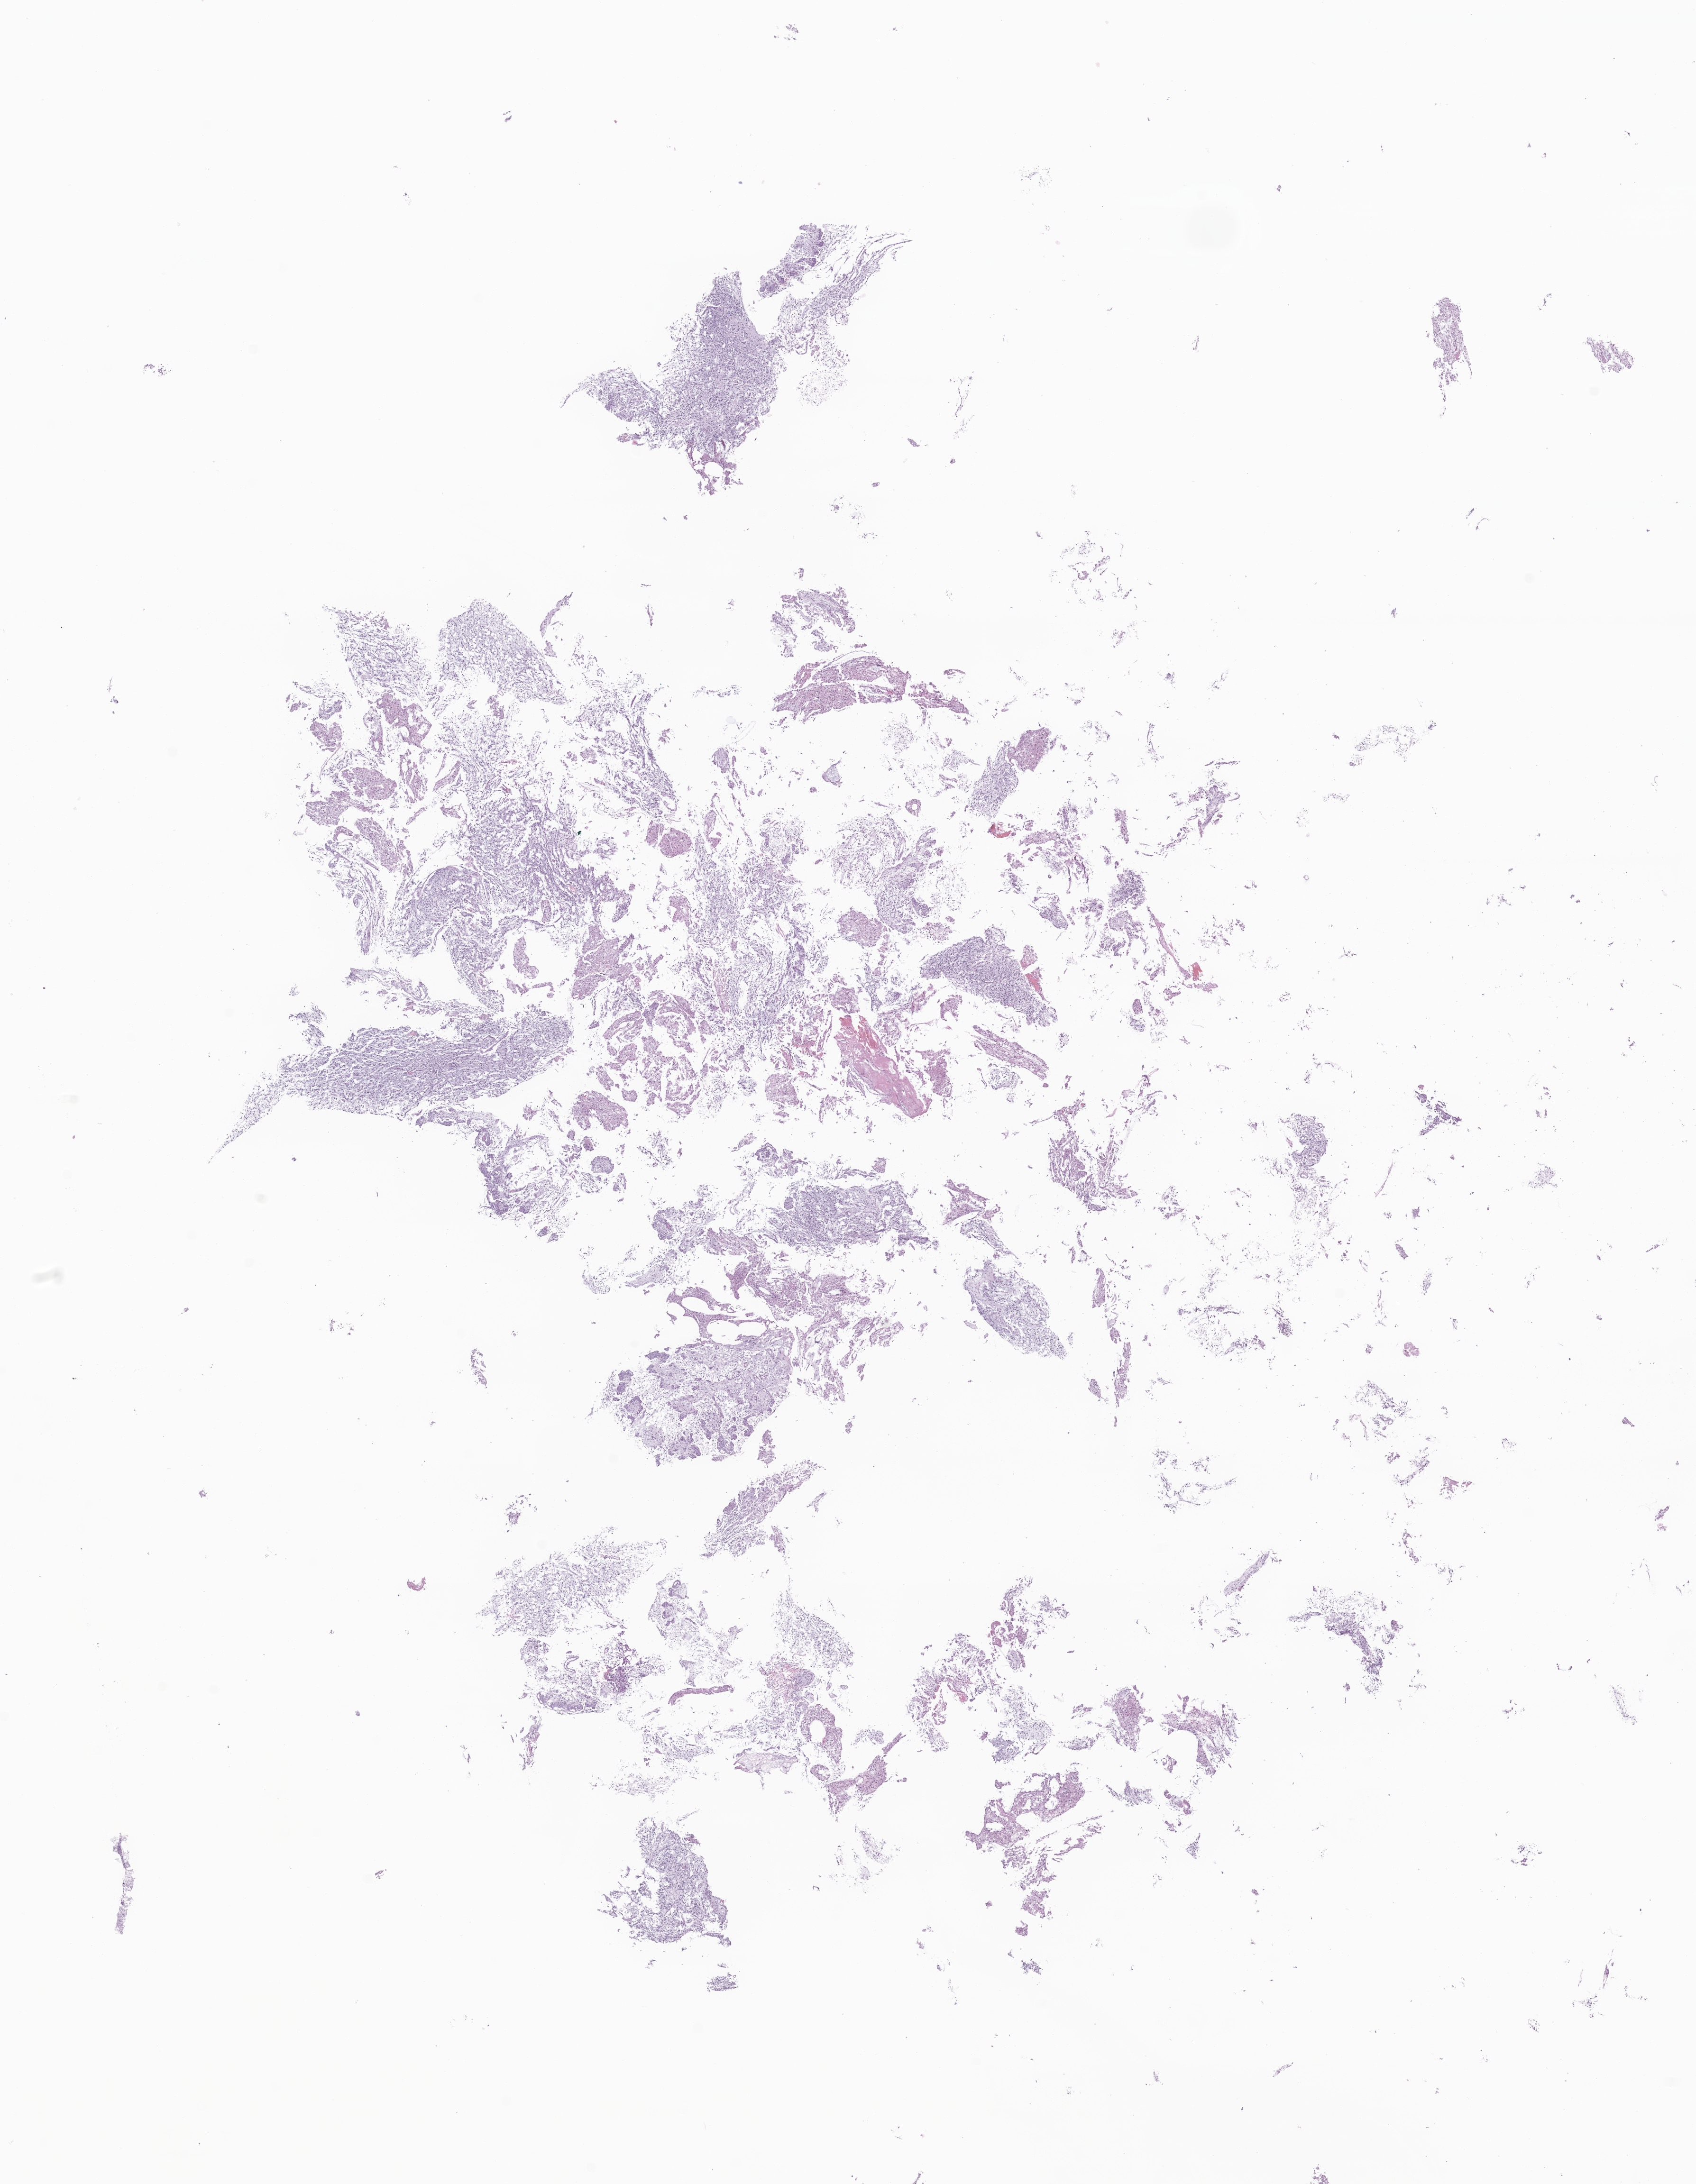
H&E whole-slide image of tumor tissue from the spinal cord, whole scanned area (about 15.1 x 19.4 mm) shown as a low-resolution overview. Formalin-fixed paraffin-embedded section. Patient: male, age 814 days (about 2.2 years).
* recorded diagnosis: Astrocytoma, NOS